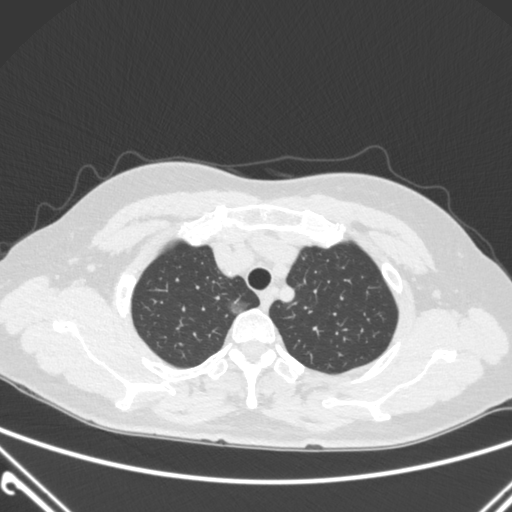
Chest CT, one axial slice; slice 238 of 300 in the series (ordered by position); 120 kVp; lung window (W 1500 / L -600 HU); 1 mm slice thickness; 512 × 512 image matrix, field of view 350 × 350 mm. Female patient, age 54 years. Case-level facts recorded for this patient, not image findings: clinical TNM (as recorded): T1a N0 M0; histopathological grade: G1.
Structures marked on this image (bounding box drawn by a radiologist):
- lung tumour (recorded histology: adenocarcinoma): box from (x=227, y=291) to (x=251, y=318) px